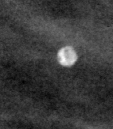
Crop from a digitized film mammogram around one marked abnormality; left breast; MLO view.
Marked abnormality: calcifications, morphology lucent center; BI-RADS assessment category 2; benign; no additional work-up was recommended (benign without callback).